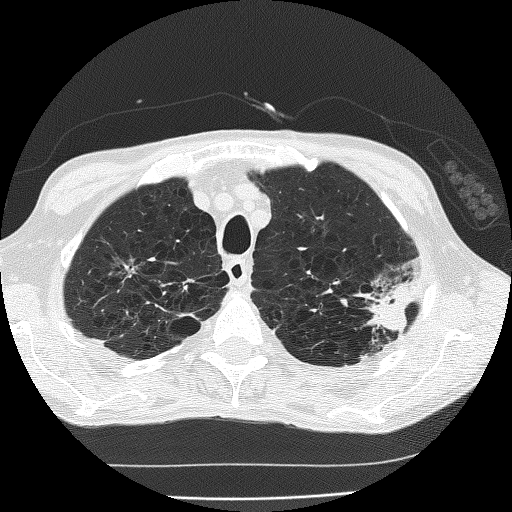
Axial slice from a low-dose chest CT screening exam; second screening round (one year after baseline); lung window (W 1500 / L -600 HU); 2 mm slice thickness; lung (sharp) reconstruction kernel (FC51); 120 kVp; 512 × 512 image matrix, field of view 320 × 320 mm. Male, age 60 years at enrolment. Current smoker at enrolment.
Expert reader's lesion annotation, box from (x=346, y=268) to (x=423, y=341) px. The screening reader recorded 2 non-calcified nodules or masses ≥4 mm on this exam; which of them this box marks is not recorded. Official screen result: positive, other.